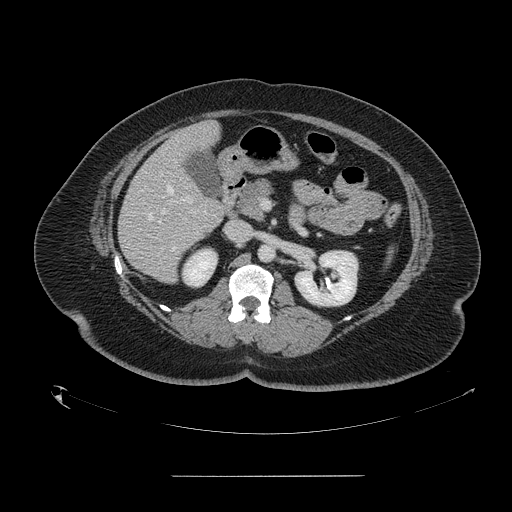
Contrast-enhanced abdominal CT, one axial slice; position 73 of 164 along the scan axis; 120 kVp; intravenous contrast given; soft-tissue window (W 400 / L 40 HU); 512 × 512 image matrix, field of view 495 × 495 mm. Female patient, age 52 years. Case-level facts recorded for this patient, not image findings: diagnosis: colorectal cancer liver metastases, imaged before liver resection; multiple liver metastases: yes; largest metastasis: 3.5 cm.
Annotated regions visible in this slice (expert manual segmentation):
- hepatic veins: bounding box <147,186,173,220> (left, top, right, bottom; pixels)
- liver: <119,122,226,282>
- planned liver remnant (the part of the liver to remain after resection): <178,122,220,153>
- portal vein (with intrahepatic branches): <161,173,189,202>